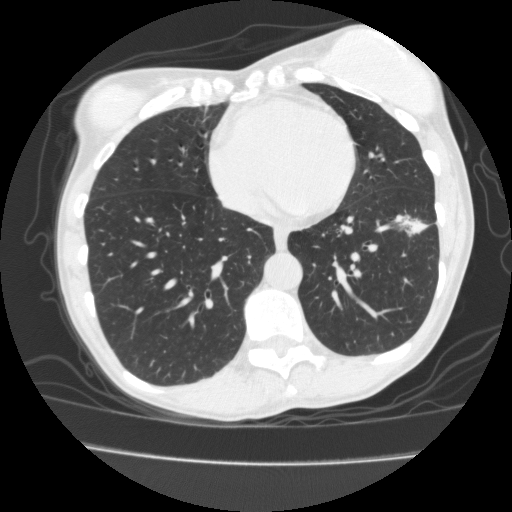
Low-dose screening chest CT, one axial slice. Position 60 of 171 along the scan axis. Reconstruction kernel FC10. 120 kVp. Lung window (W 1500 / L -600 HU). 512 × 512 image matrix.
Outlined on this slice (manually delineated by an expert):
- lesion 1 (tumor, lower lobe of left lung): bounding box [x1, y1, x2, y2] px = [405, 219, 426, 234]